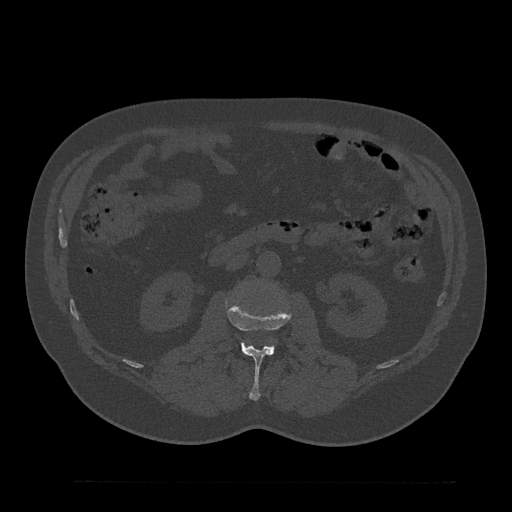
CT including the spine, one axial slice; position 85 of 797 along the scan axis; reconstruction kernel Br40s/3; 120 kVp; bone window (W 1800 / L 400 HU); 0.5 mm slice thickness; 512 × 512 image matrix, field of view 430 × 430 mm. Patient: male, 61 years. Case-level facts recorded for this patient, not image findings: primary cancer: prostate.
Outlined on this slice (semi-automatically segmented with operator editing):
- L2 vertebra: bounding box <226,301,291,400> (left, top, right, bottom; pixels)